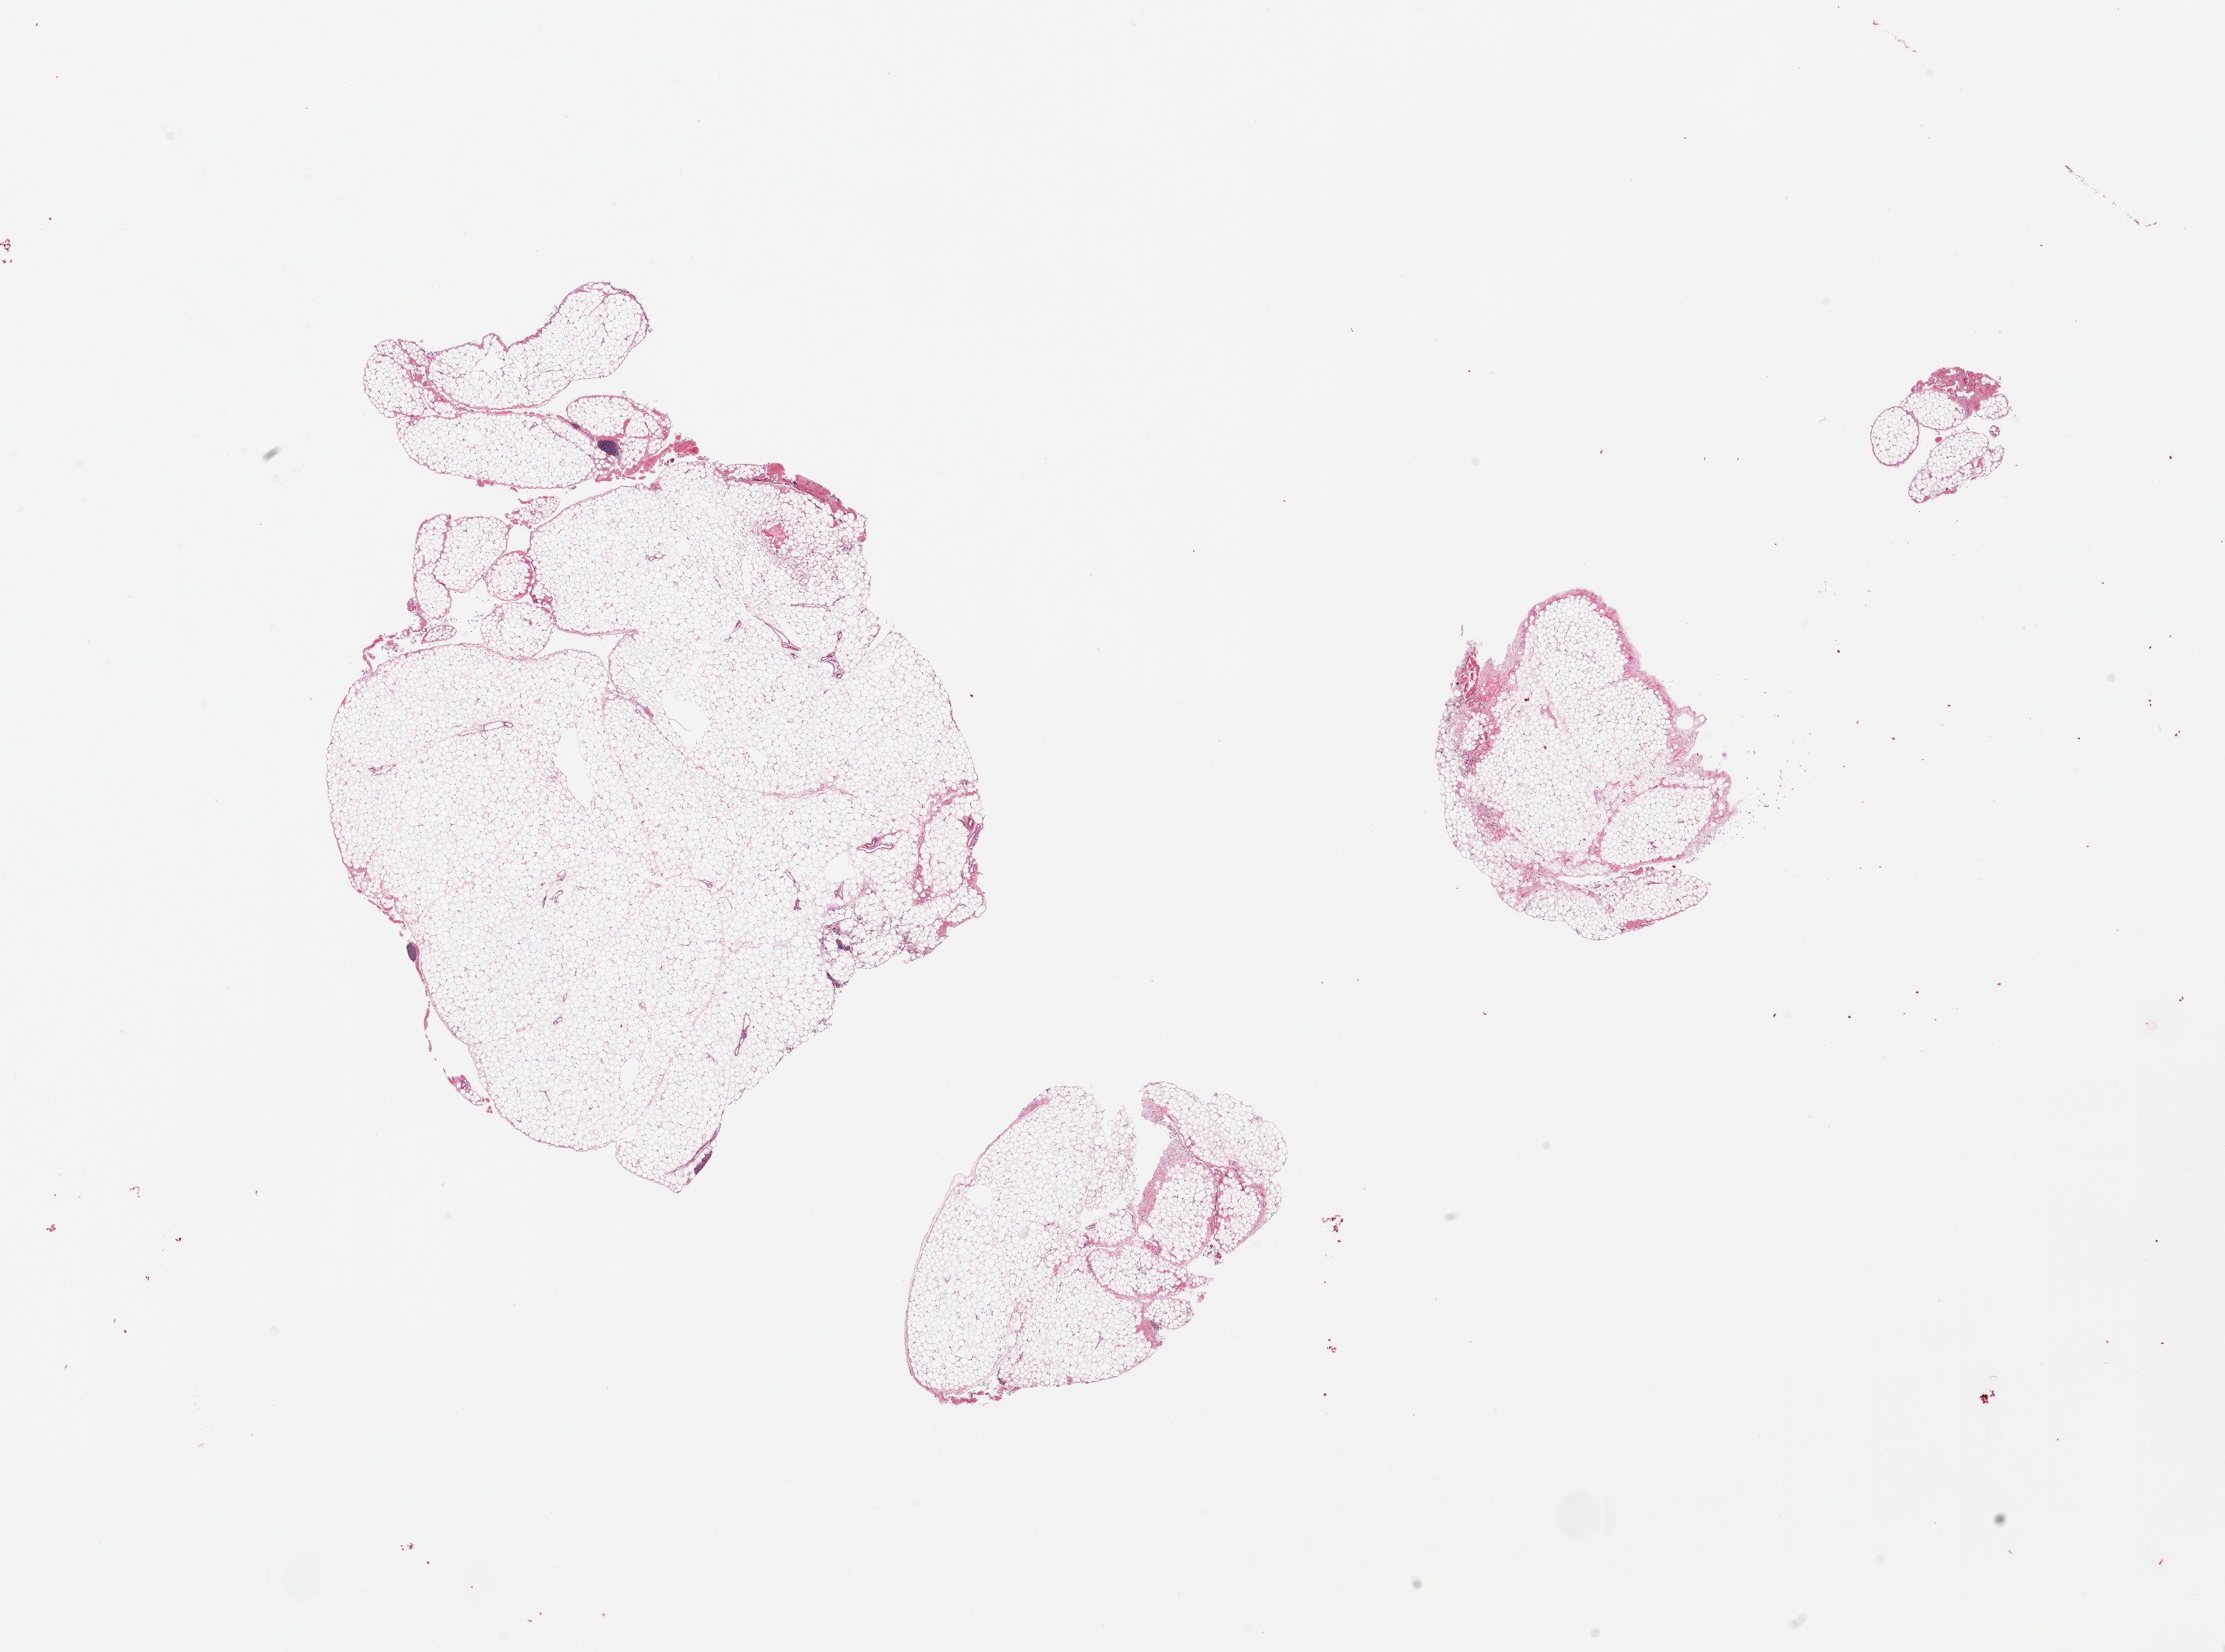
Digitized hematoxylin and eosin (H&E)-stained section, whole scanned area (about 24.6 x 18.3 mm) shown as a low-resolution overview. PAXgene-fixed paraffin-embedded (PFPE) section. Target tissue: omentum. Donor tissue sample. Donor sex: female.
- review note (as recorded): 2 pieces, trace fascia